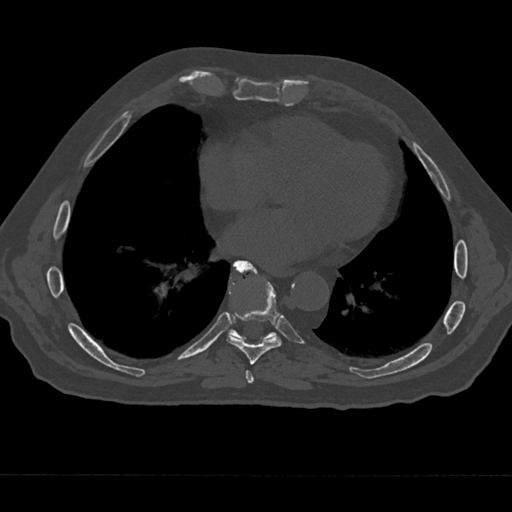
CT including the spine, one axial slice. Slice 301 of 797 in the series (ordered by position). Reconstruction kernel Br40s/3. Bone window (W 1800 / L 400 HU). 512 × 512 image matrix, field of view 377 × 377 mm. Male patient, age 75 years. Case-level facts recorded for this patient, not image findings: primary cancer: renal.
Outlined on this slice (semi-automatic segmentation, software-assisted and operator-edited):
- T7 vertebra: bounding box <241,368,255,385> (left, top, right, bottom; pixels)
- T8 vertebra: <227,263,282,365>
- T9 vertebra: <228,260,277,340>